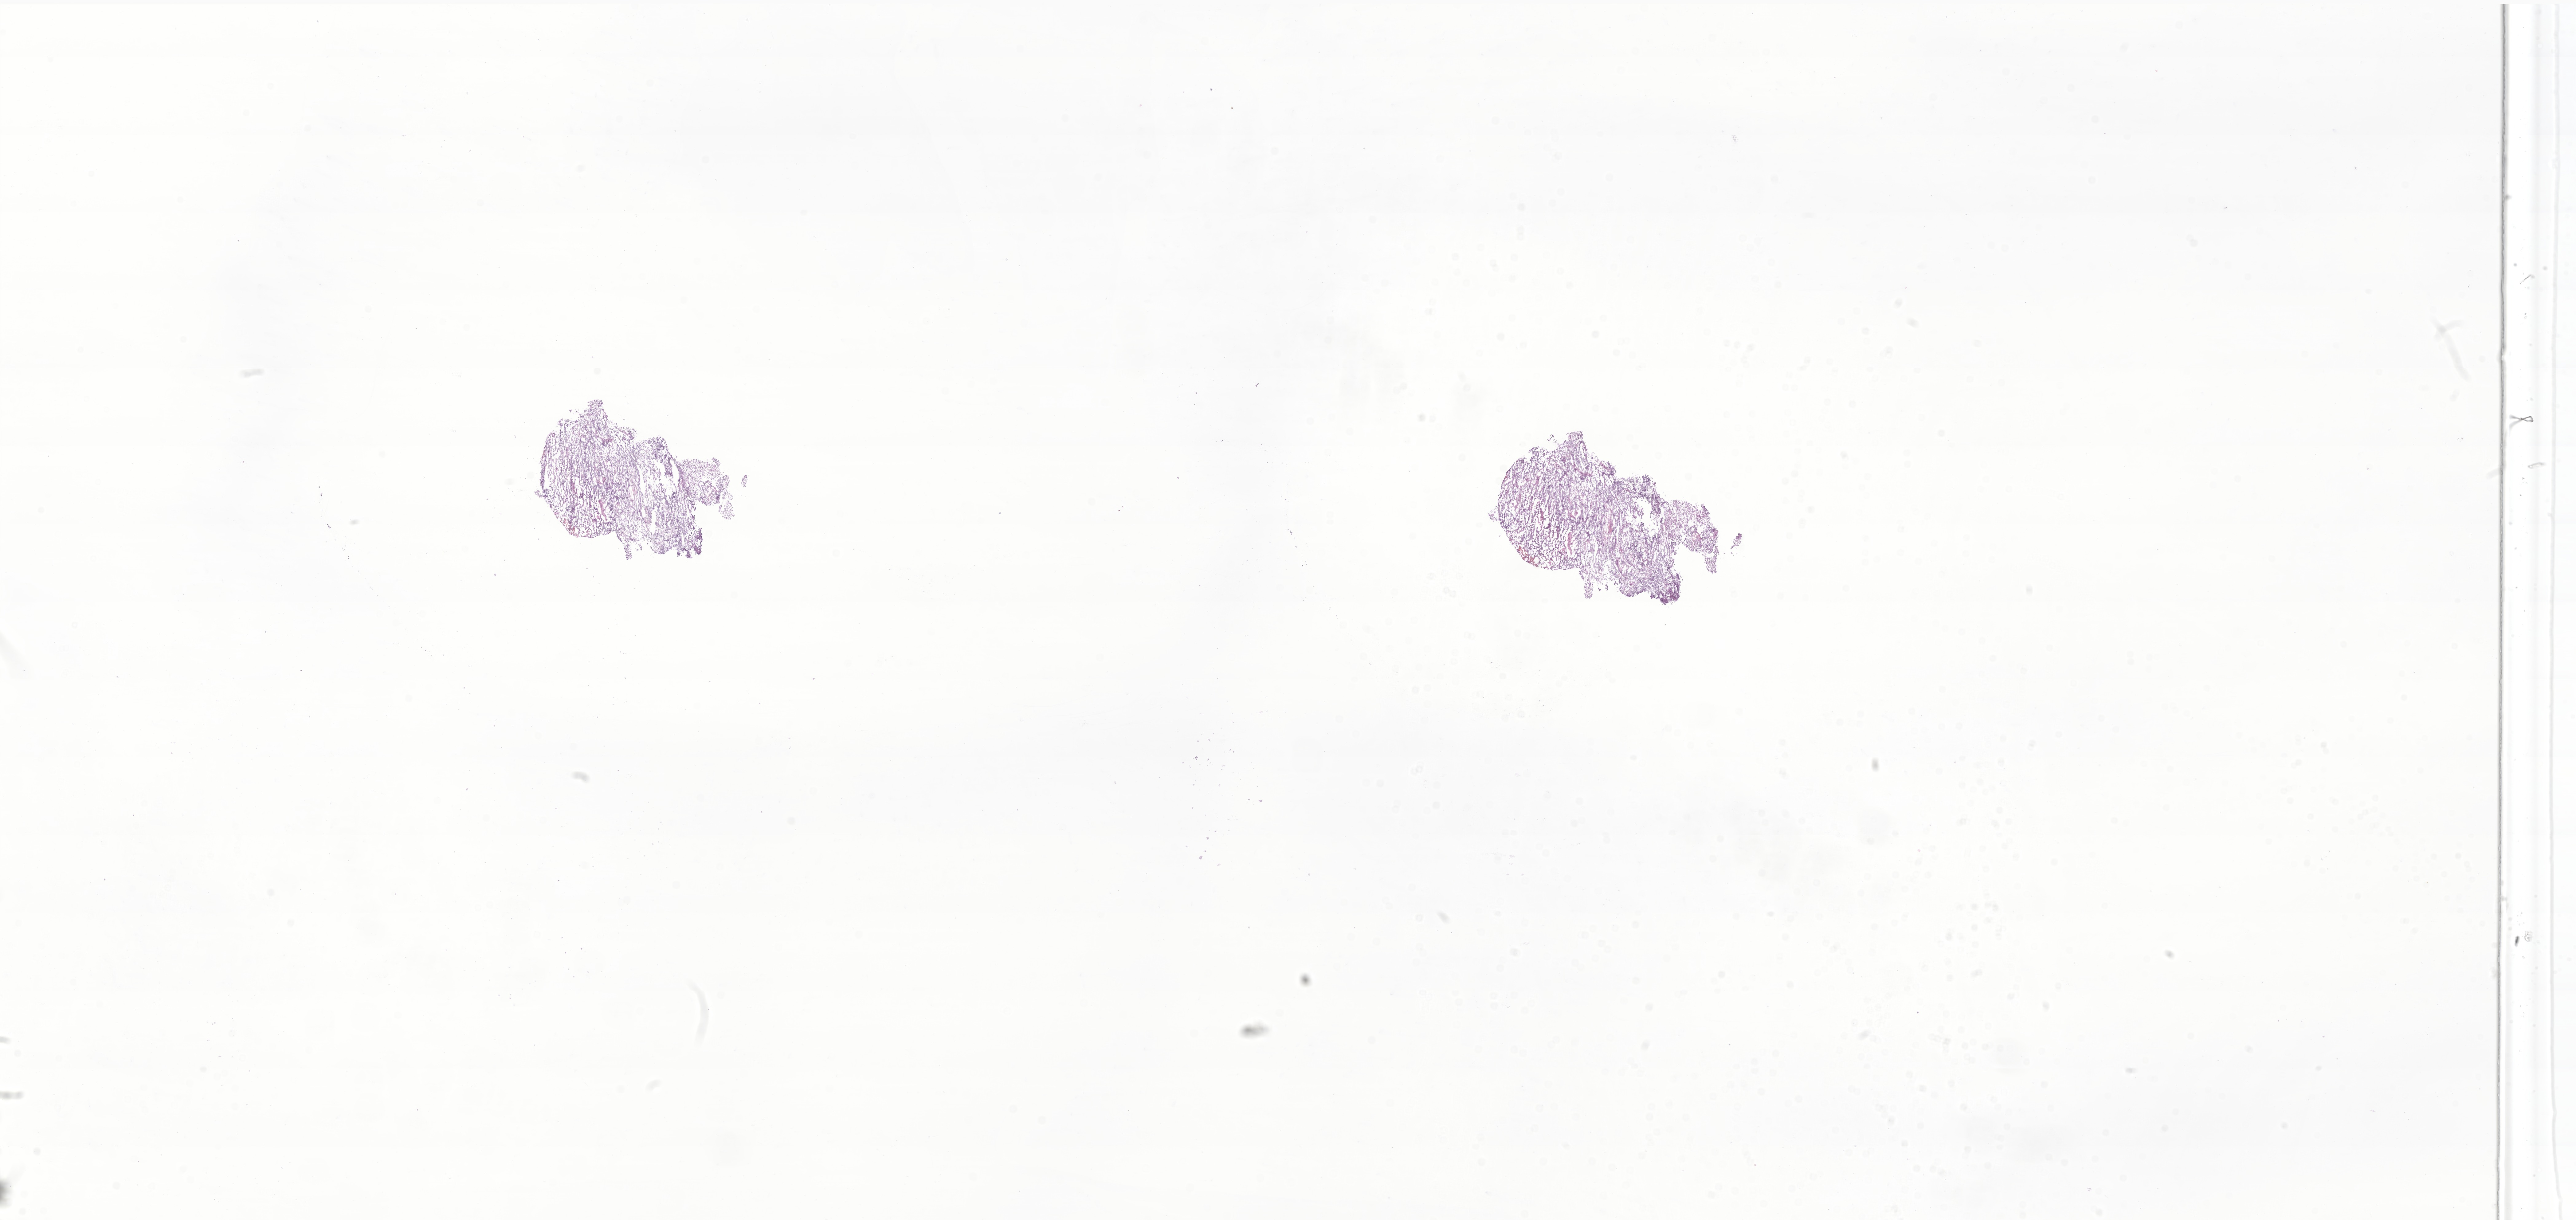
Whole-slide image, haematoxylin and eosin stain of tumor tissue from the spinal meninges — shown as a low-resolution overview of the whole scanned area (about 35.4 x 16.7 mm), cryosection (OCT / tissue freezing medium). Female patient, age 153 months (12 years 9 months).
Diagnosis: Ependymoma, NOS.